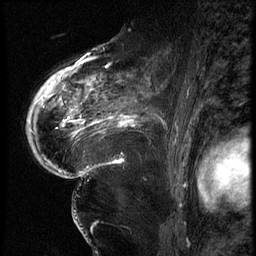
Breast MRI (dynamic contrast-enhanced), one sagittal slice. Slice 42 of 62 in the series (ordered by position). 3 images stored at this slice position (order not interpretable as contrast timing). 1.5 T. TE 4.2 ms, TR 9 ms. 2.5 mm slice thickness. 256 × 256 image matrix. Patient: female, 56 years. Case-level facts recorded for this patient, not image findings: setting: breast cancer imaged before/during neoadjuvant chemotherapy; receptor status: HER2-positive.
Annotated regions visible in this slice (semi-automatic segmentation, software-assisted and operator-edited):
- analysis volume of interest (the breast-tissue region the enhancement analysis was run in; not a lesion): bounding box (x1, y1, x2, y2) in pixels: (84, 75, 181, 153)
- tumour enhancement mask (voxels above the 140 % enhancement threshold inside the analysis volume of interest): (84, 76, 137, 137)